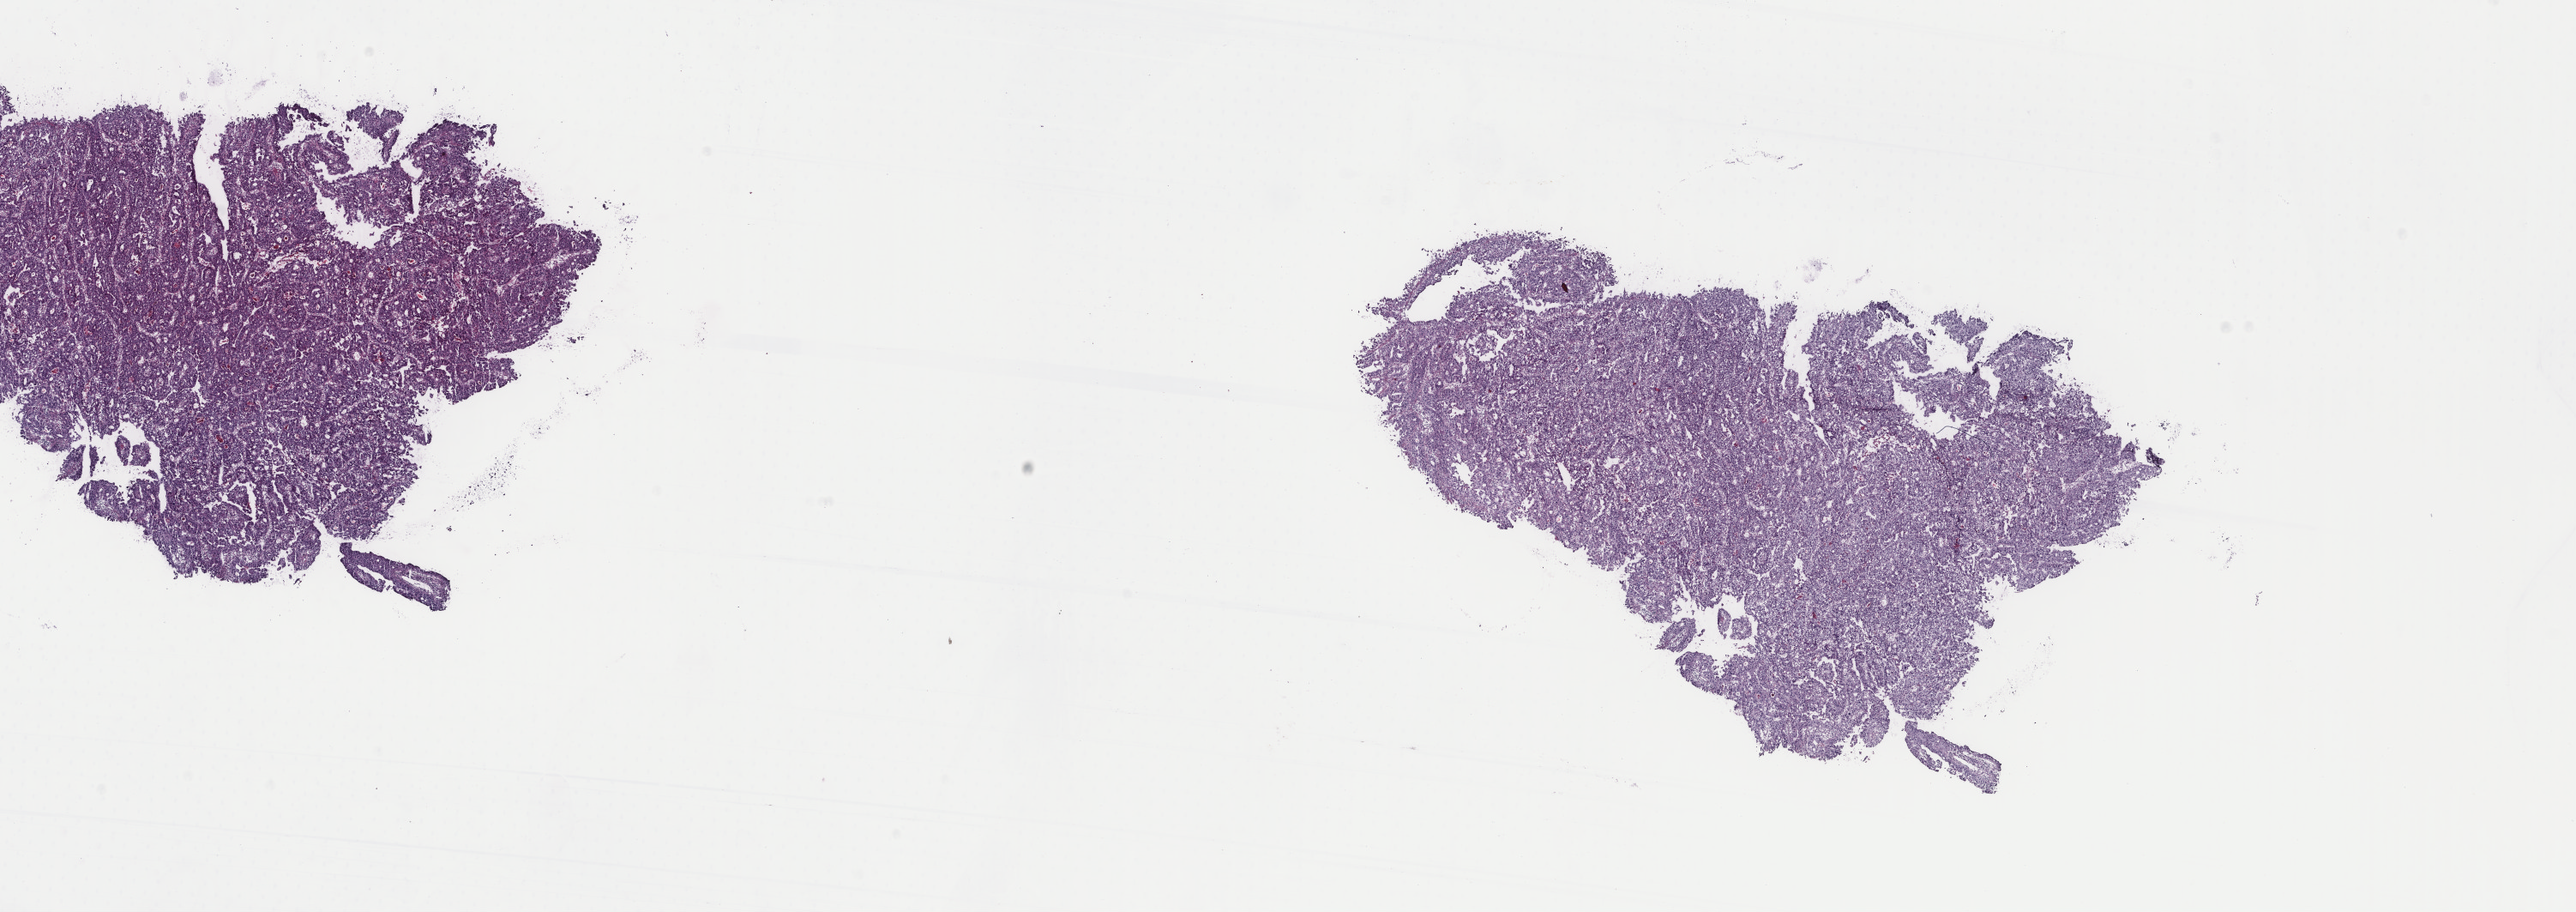
Whole-slide histology image, Hematoxylin and eosin (H&E) stained — low-resolution overview of the scanned area, about 23.8 x 8.4 mm, frozen section from the top of the tissue portion, stomach, primary tumour sample. Male patient; age at initial diagnosis 74 years. Histologic grade: G3 (poorly differentiated). Slide review estimates, as recorded: tumour cells 99%, tumour nuclei 83%, normal cells 0%, stromal cells 0%, necrosis 1%. Inflammatory infiltration, as recorded: lymphocyte infiltration 2%, monocyte infiltration 0%, neutrophil infiltration 0%.
Pathologic diagnosis: Papillary adenocarcinoma, NOS (cardia, NOS). AJCC pathologic stage: IA (7th edition).